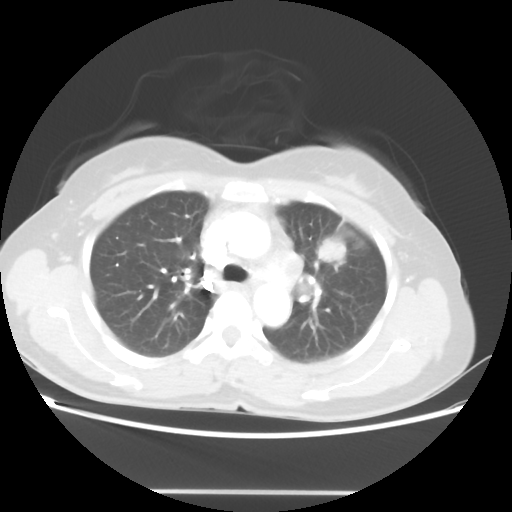
Chest CT, one axial slice. Position 32 of 46 along the scan axis. Reconstruction kernel STANDARD. 100 kVp. Lung window (W 1500 / L -600 HU). 5 mm slice thickness. 512 × 512 image matrix, field of view 360 × 360 mm. Female patient, age 50 years. From the clinical record (not read from this slice): clinical TNM (as recorded): T1c N1 M0.
Structures marked on this image (rectangle marked by the reading radiologist):
- lung tumour (recorded histology: adenocarcinoma): bounding box [x1, y1, x2, y2] px = [318, 240, 346, 261]